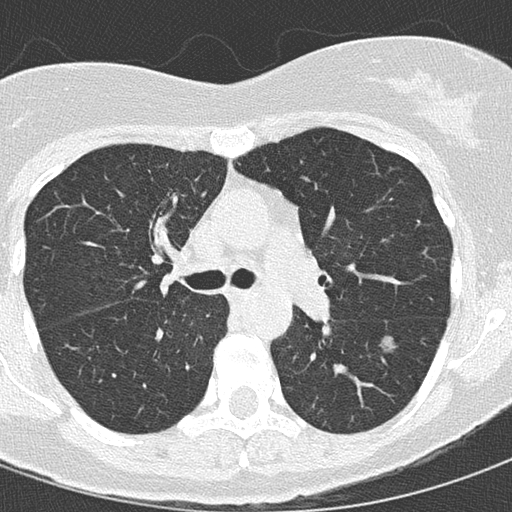
Low-dose screening chest CT, axial slice; baseline screening round; lung window (W 1500 / L -600 HU); 2 mm slice thickness; slice 53 of 145 in the series. Female, age 68 years at enrolment. Current smoker at enrolment.
Expert-annotated lung lesion, box from (x=372, y=325) to (x=417, y=365) px. Reader record for this screening exam (exam-level; its link to the box is not recorded): non-calcified nodule or mass ≥4 mm, left lower lobe, 15 × 15 mm, mixed attenuation. Later outcome: lung cancer diagnosed 72 days after this screen — bronchiolo-alveolar adenocarcinoma, NOS, left lower lobe, stage IIIB (AJCC 6th edition), 12 mm at pathology.